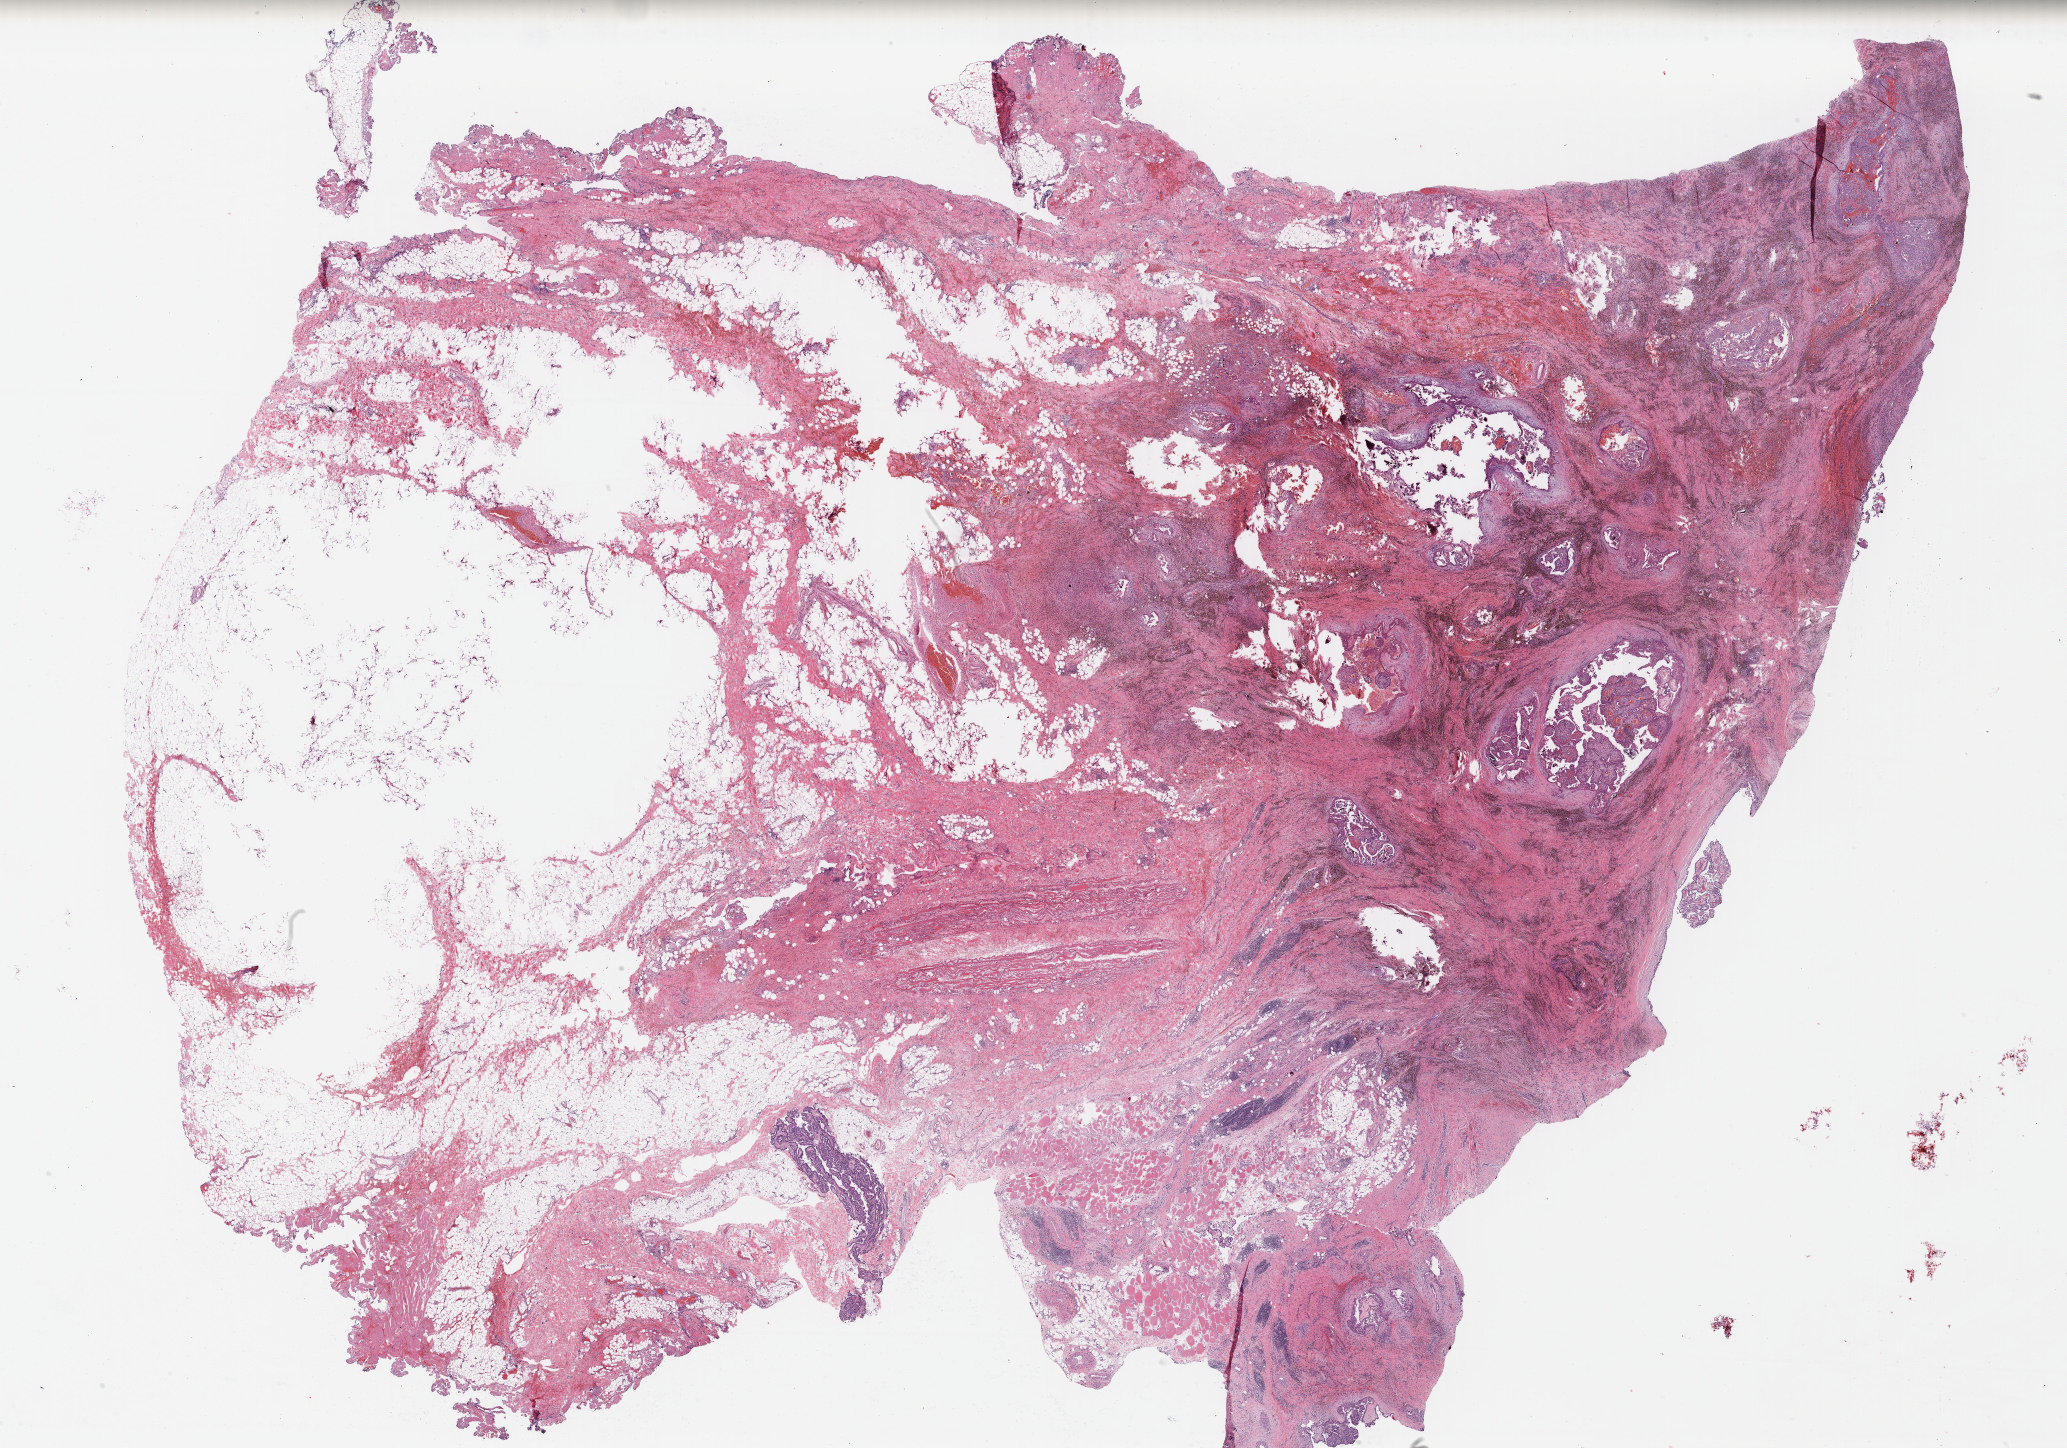
Whole-slide histology image, Hematoxylin and eosin (H&E) stained, shown as a low-resolution overview of the whole scanned area (about 32.5 x 22.8 mm, from a 40x scan); formalin-fixed paraffin-embedded (FFPE) diagnostic section; thyroid, primary tumour sample. Male patient; age at initial diagnosis 35 years.
* AJCC pathologic stage: I (7th edition)
* TNM: T3 N1b M0
* histologic diagnosis: Papillary adenocarcinoma, NOS
* lymph nodes positive (case pathology): 40 of 77 examined